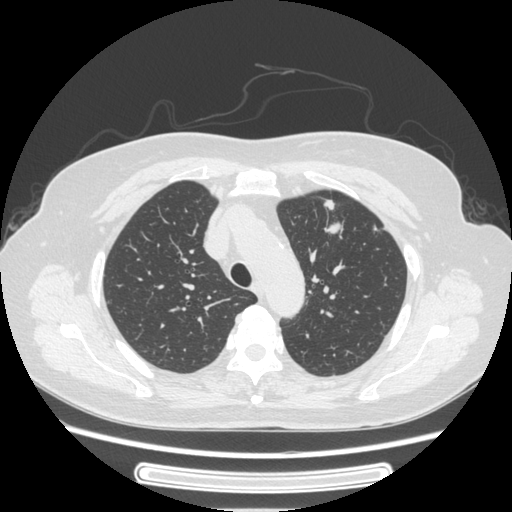
Chest CT, one axial slice. Lung window (W 1500 / L -600 HU). 512 × 512 image matrix, field of view 363 × 363 mm. Female patient, age 77 years. From the clinical record (not read from this slice): clinical TNM (as recorded): T1c N3 M0; histopathological grade: G2-3.
Structures marked on this image (bounding box drawn by a radiologist):
- lung tumour (recorded histology: adenocarcinoma): box from (x=322, y=190) to (x=343, y=238) px